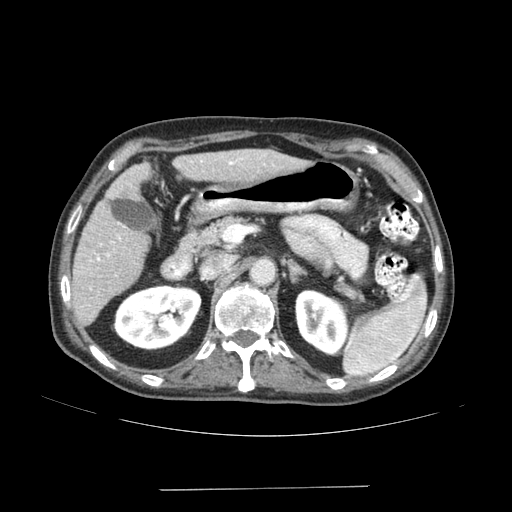
Contrast-enhanced abdominal CT (liver protocol), one axial slice; slice 80 of 192 in the series (ordered by position); soft-tissue window (W 400 / L 40 HU); 2.5 mm slice thickness; 512 × 512 image matrix, field of view 400 × 400 mm. From the clinical record (not read from this slice): diagnosis: hepatocellular carcinoma (patient treated with transarterial chemoembolisation; whether this scan precedes or follows treatment is not stated here); TNM stage (as recorded): Stage-IVA; Child-Pugh class: A; tumour differentiation: poorly differentiated; tumour nodularity: uninodular.
Structures marked on this image (semi-automatically segmented with operator editing):
- liver parenchyma outside the tumour (the mass and vessels are separate outlines, so this box may not span the whole liver): bounding box <72,150,307,325> (left, top, right, bottom; pixels)
- liver vessels: <97,161,235,260>